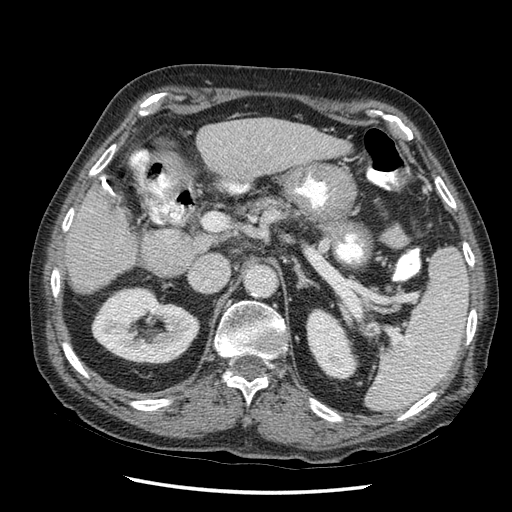
Contrast-enhanced abdominal CT (liver protocol), one axial slice. Slice 21 of 67 in the series (ordered by position). Reconstruction kernel STANDARD. 120 kVp. Soft-tissue window (W 400 / L 40 HU). 512 × 512 image matrix. Case-level facts recorded for this patient, not image findings: diagnosis: hepatocellular carcinoma (patient treated with transarterial chemoembolisation; whether this scan precedes or follows treatment is not stated here); TNM stage (as recorded): Stage-I; Child-Pugh class: A; tumour differentiation: moderately differentiated; tumour nodularity: uninodular.
Outlined on this slice (semi-automatically segmented with operator editing):
- liver parenchyma outside the tumour (the mass and vessels are separate outlines, so this box may not span the whole liver): bounding box [x1, y1, x2, y2] px = [66, 118, 346, 293]
- liver vessels: [91, 190, 121, 246]